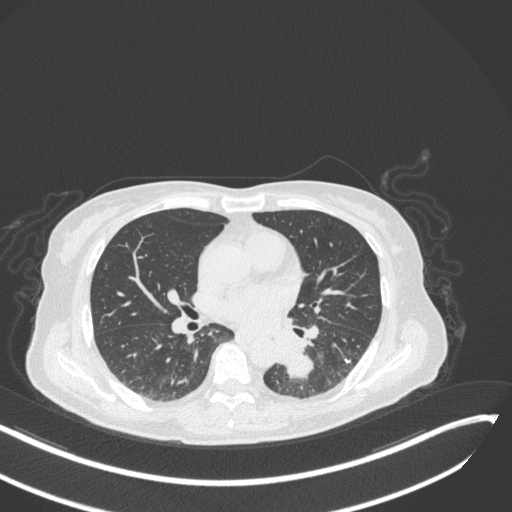
Chest CT, one axial slice. Reconstruction kernel B31f. 120 kVp. Lung window (W 1500 / L -600 HU). 512 × 512 image matrix, field of view 400 × 400 mm. Female patient, age 64 years. Case-level facts recorded for this patient, not image findings: clinical TNM (as recorded): T3 N1 M1.
Structures marked on this image (rectangle marked by the reading radiologist):
- lung tumour (recorded histology: small cell carcinoma): bounding box <276,348,318,389> (left, top, right, bottom; pixels)